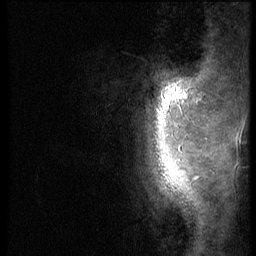
Breast MRI (dynamic contrast-enhanced), one sagittal slice; position 7 of 56 along the scan axis; 3 images stored at this slice position (order not interpretable as contrast timing); 1.5 T; TE 4.2 ms, TR 9 ms; 2.5 mm slice thickness; 256 × 256 image matrix, field of view 180 × 180 mm. Female patient, age 46 years. Case-level facts recorded for this patient, not image findings: setting: breast cancer imaged before/during neoadjuvant chemotherapy; receptor status: HER2-positive.
Structures marked on this image (semi-automatically segmented with operator editing):
- analysis volume of interest (the breast-tissue region the enhancement analysis was run in; not a lesion): box from (x=114, y=68) to (x=190, y=143) px
- tumour enhancement mask (voxels above the 140 % enhancement threshold inside the analysis volume of interest): (x=179, y=94)–(x=186, y=98)